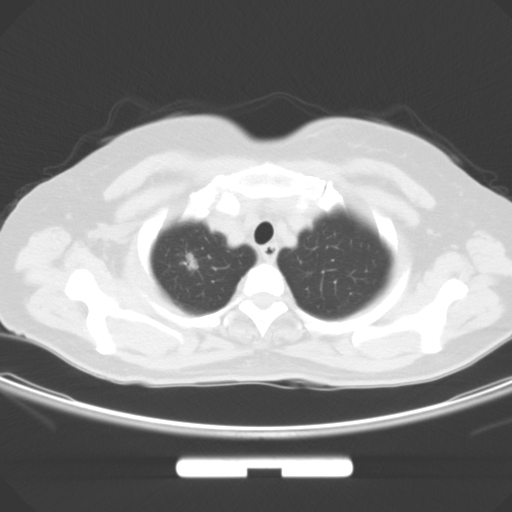
Chest CT, one axial slice. Position 52 of 59 along the scan axis. 120 kVp. Lung window (W 1500 / L -600 HU). 512 × 512 image matrix, field of view 369 × 369 mm. Female patient, age 58 years. From the clinical record (not read from this slice): clinical TNM (as recorded): T1b N0 M0; histopathological grade: G2-3.
Outlined on this slice (rectangle marked by the reading radiologist):
- lung tumour (recorded histology: adenocarcinoma): bounding box <181,252,201,280> (left, top, right, bottom; pixels)